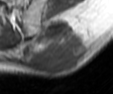
MRI of an extremity soft-tissue mass, one axial slice; slice 23 of 42 in the series (ordered by position); MR volume resampled by the dataset authors to the PET/CT grid (not the native acquisition matrix); 3.27 mm slice thickness; 113 × 94 image matrix. Male patient. Case-level facts recorded for this patient, not image findings: histological type: leiomyosarcoma; grade: intermediate; site of the primary tumour: left pelvis.
Outlined on this slice (expert contour drawn on MRI and transferred to this co-registered scan by the dataset authors):
- gross tumour volume (mass): bounding box <22,18,91,74> (left, top, right, bottom; pixels)